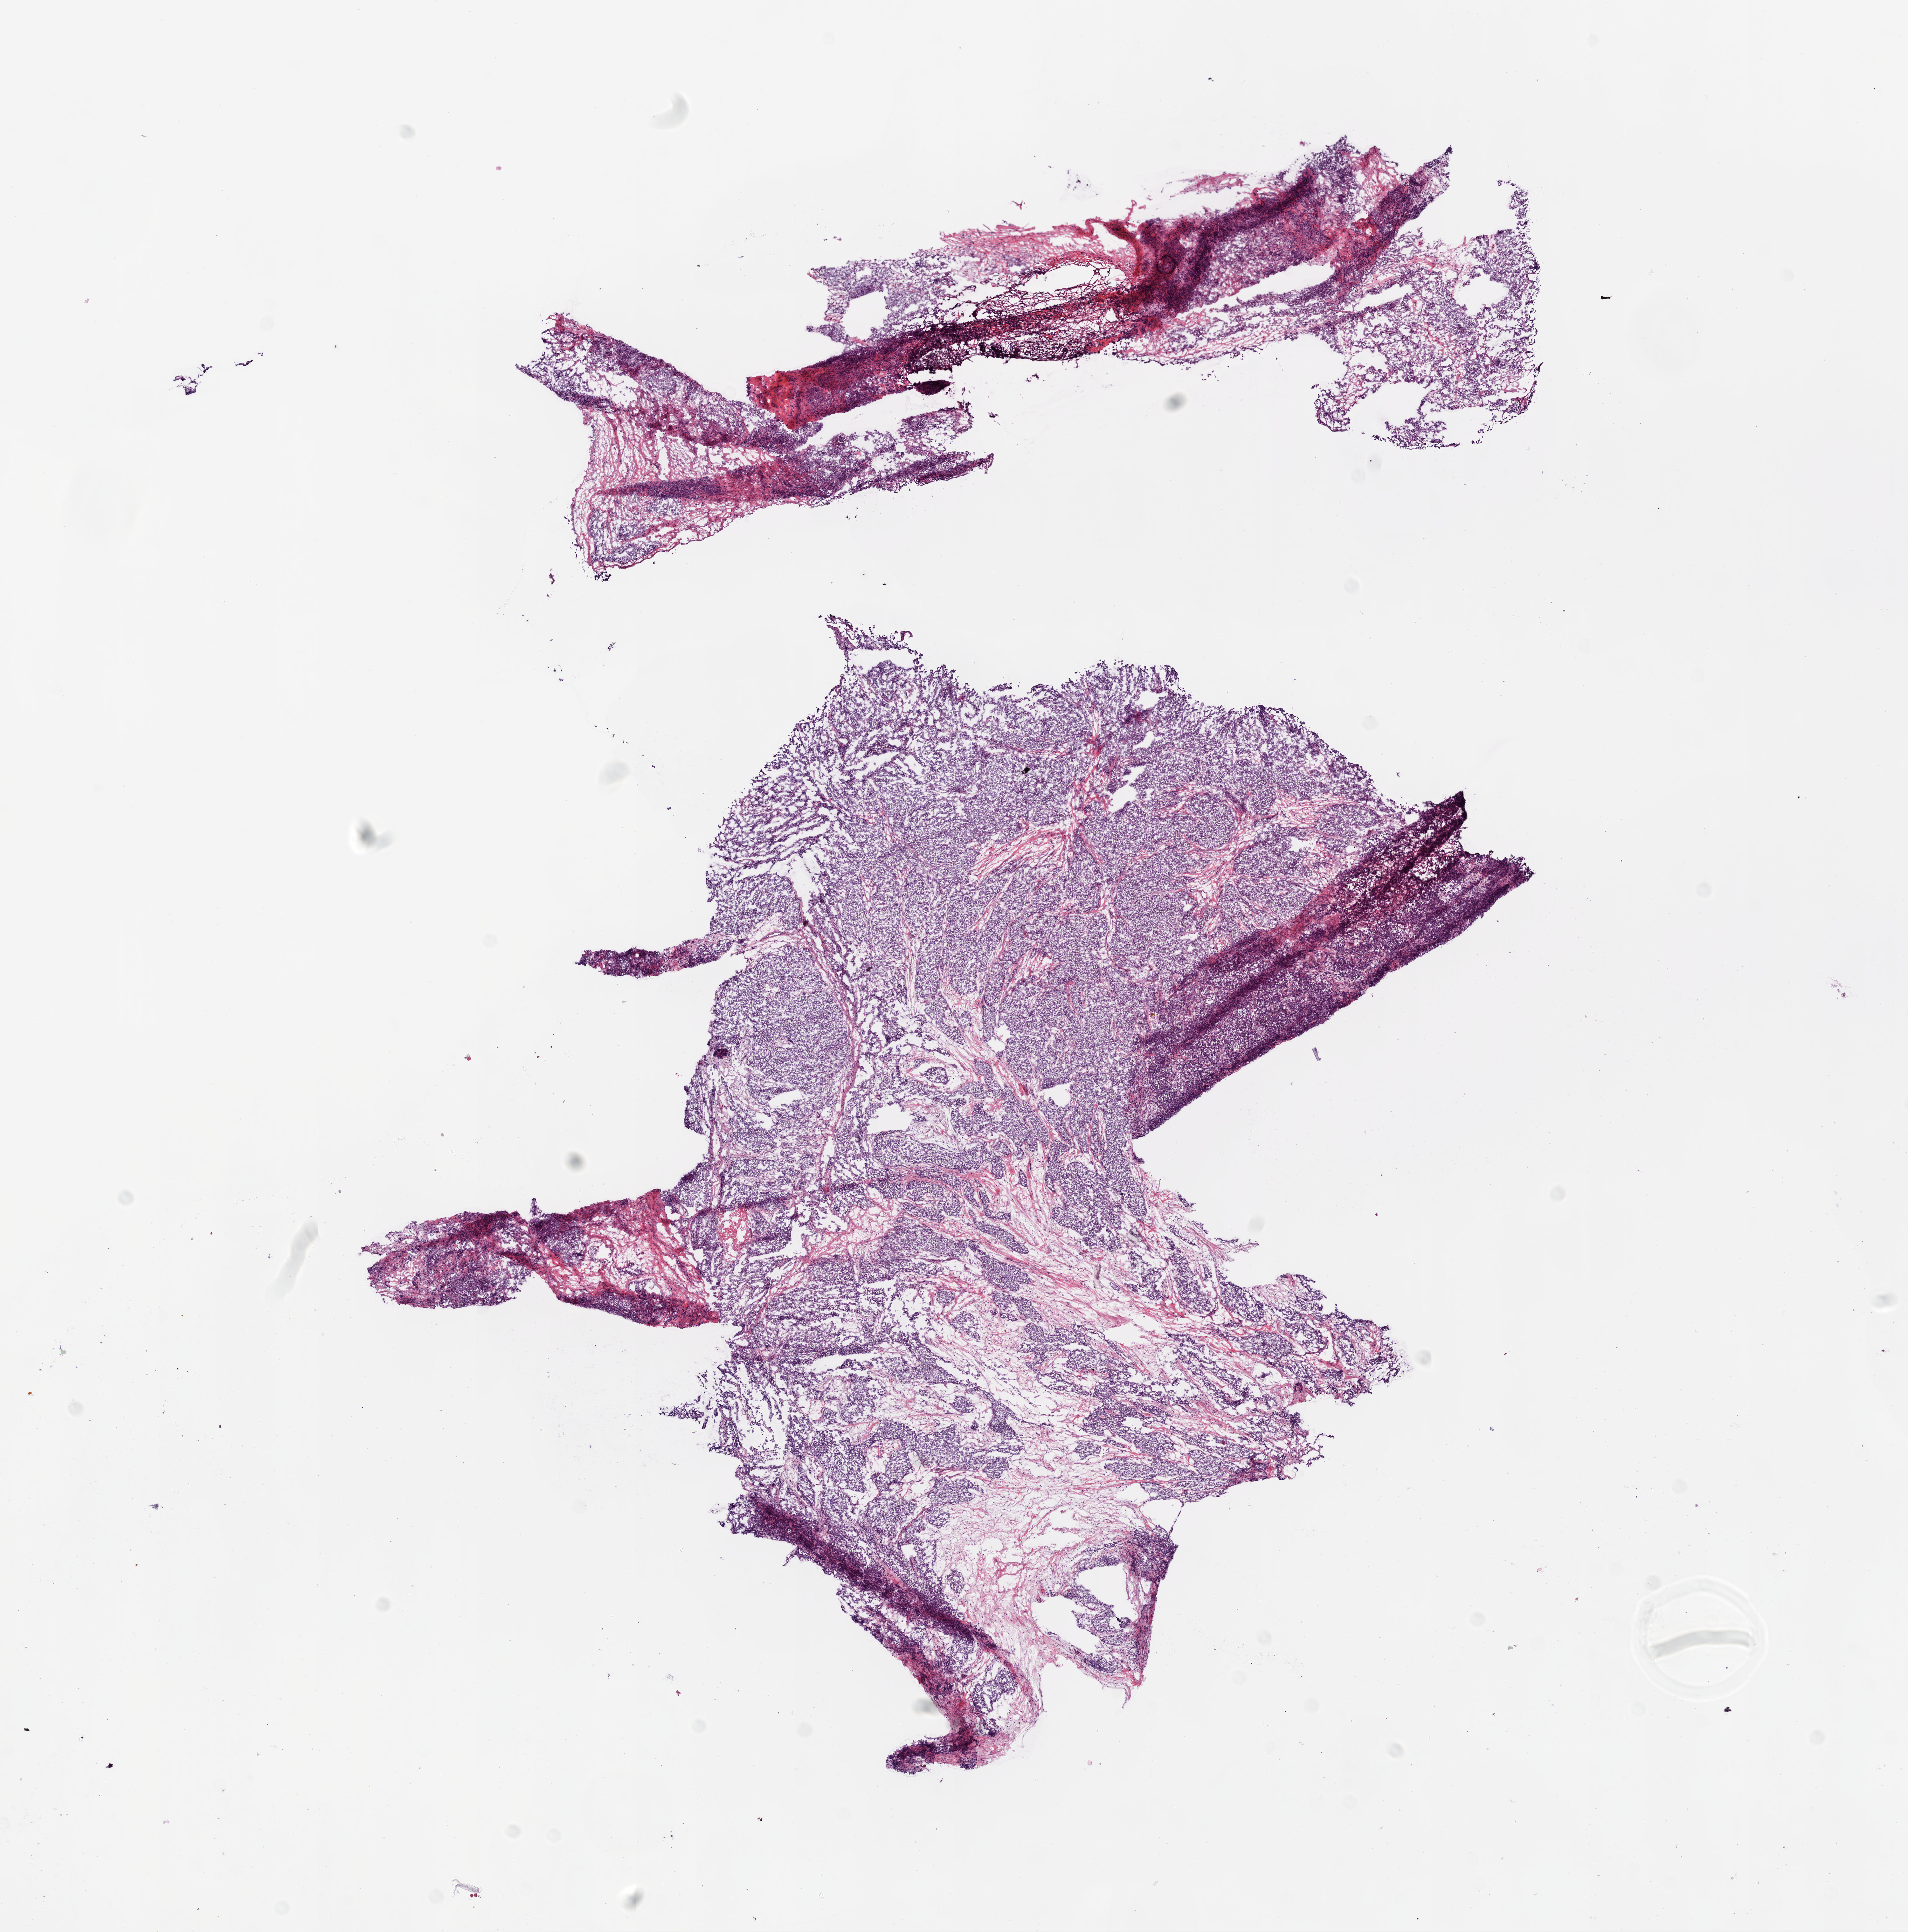
Digitized H&E-stained tissue section (whole slide) — a low-resolution overview of the entire scanned area, about 12.0 x 12.2 mm, frozen section, primary tumour sample from the ovary. Patient: female, age at initial diagnosis 66 years.
Pathologic diagnosis: Serous cystadenocarcinoma, NOS.